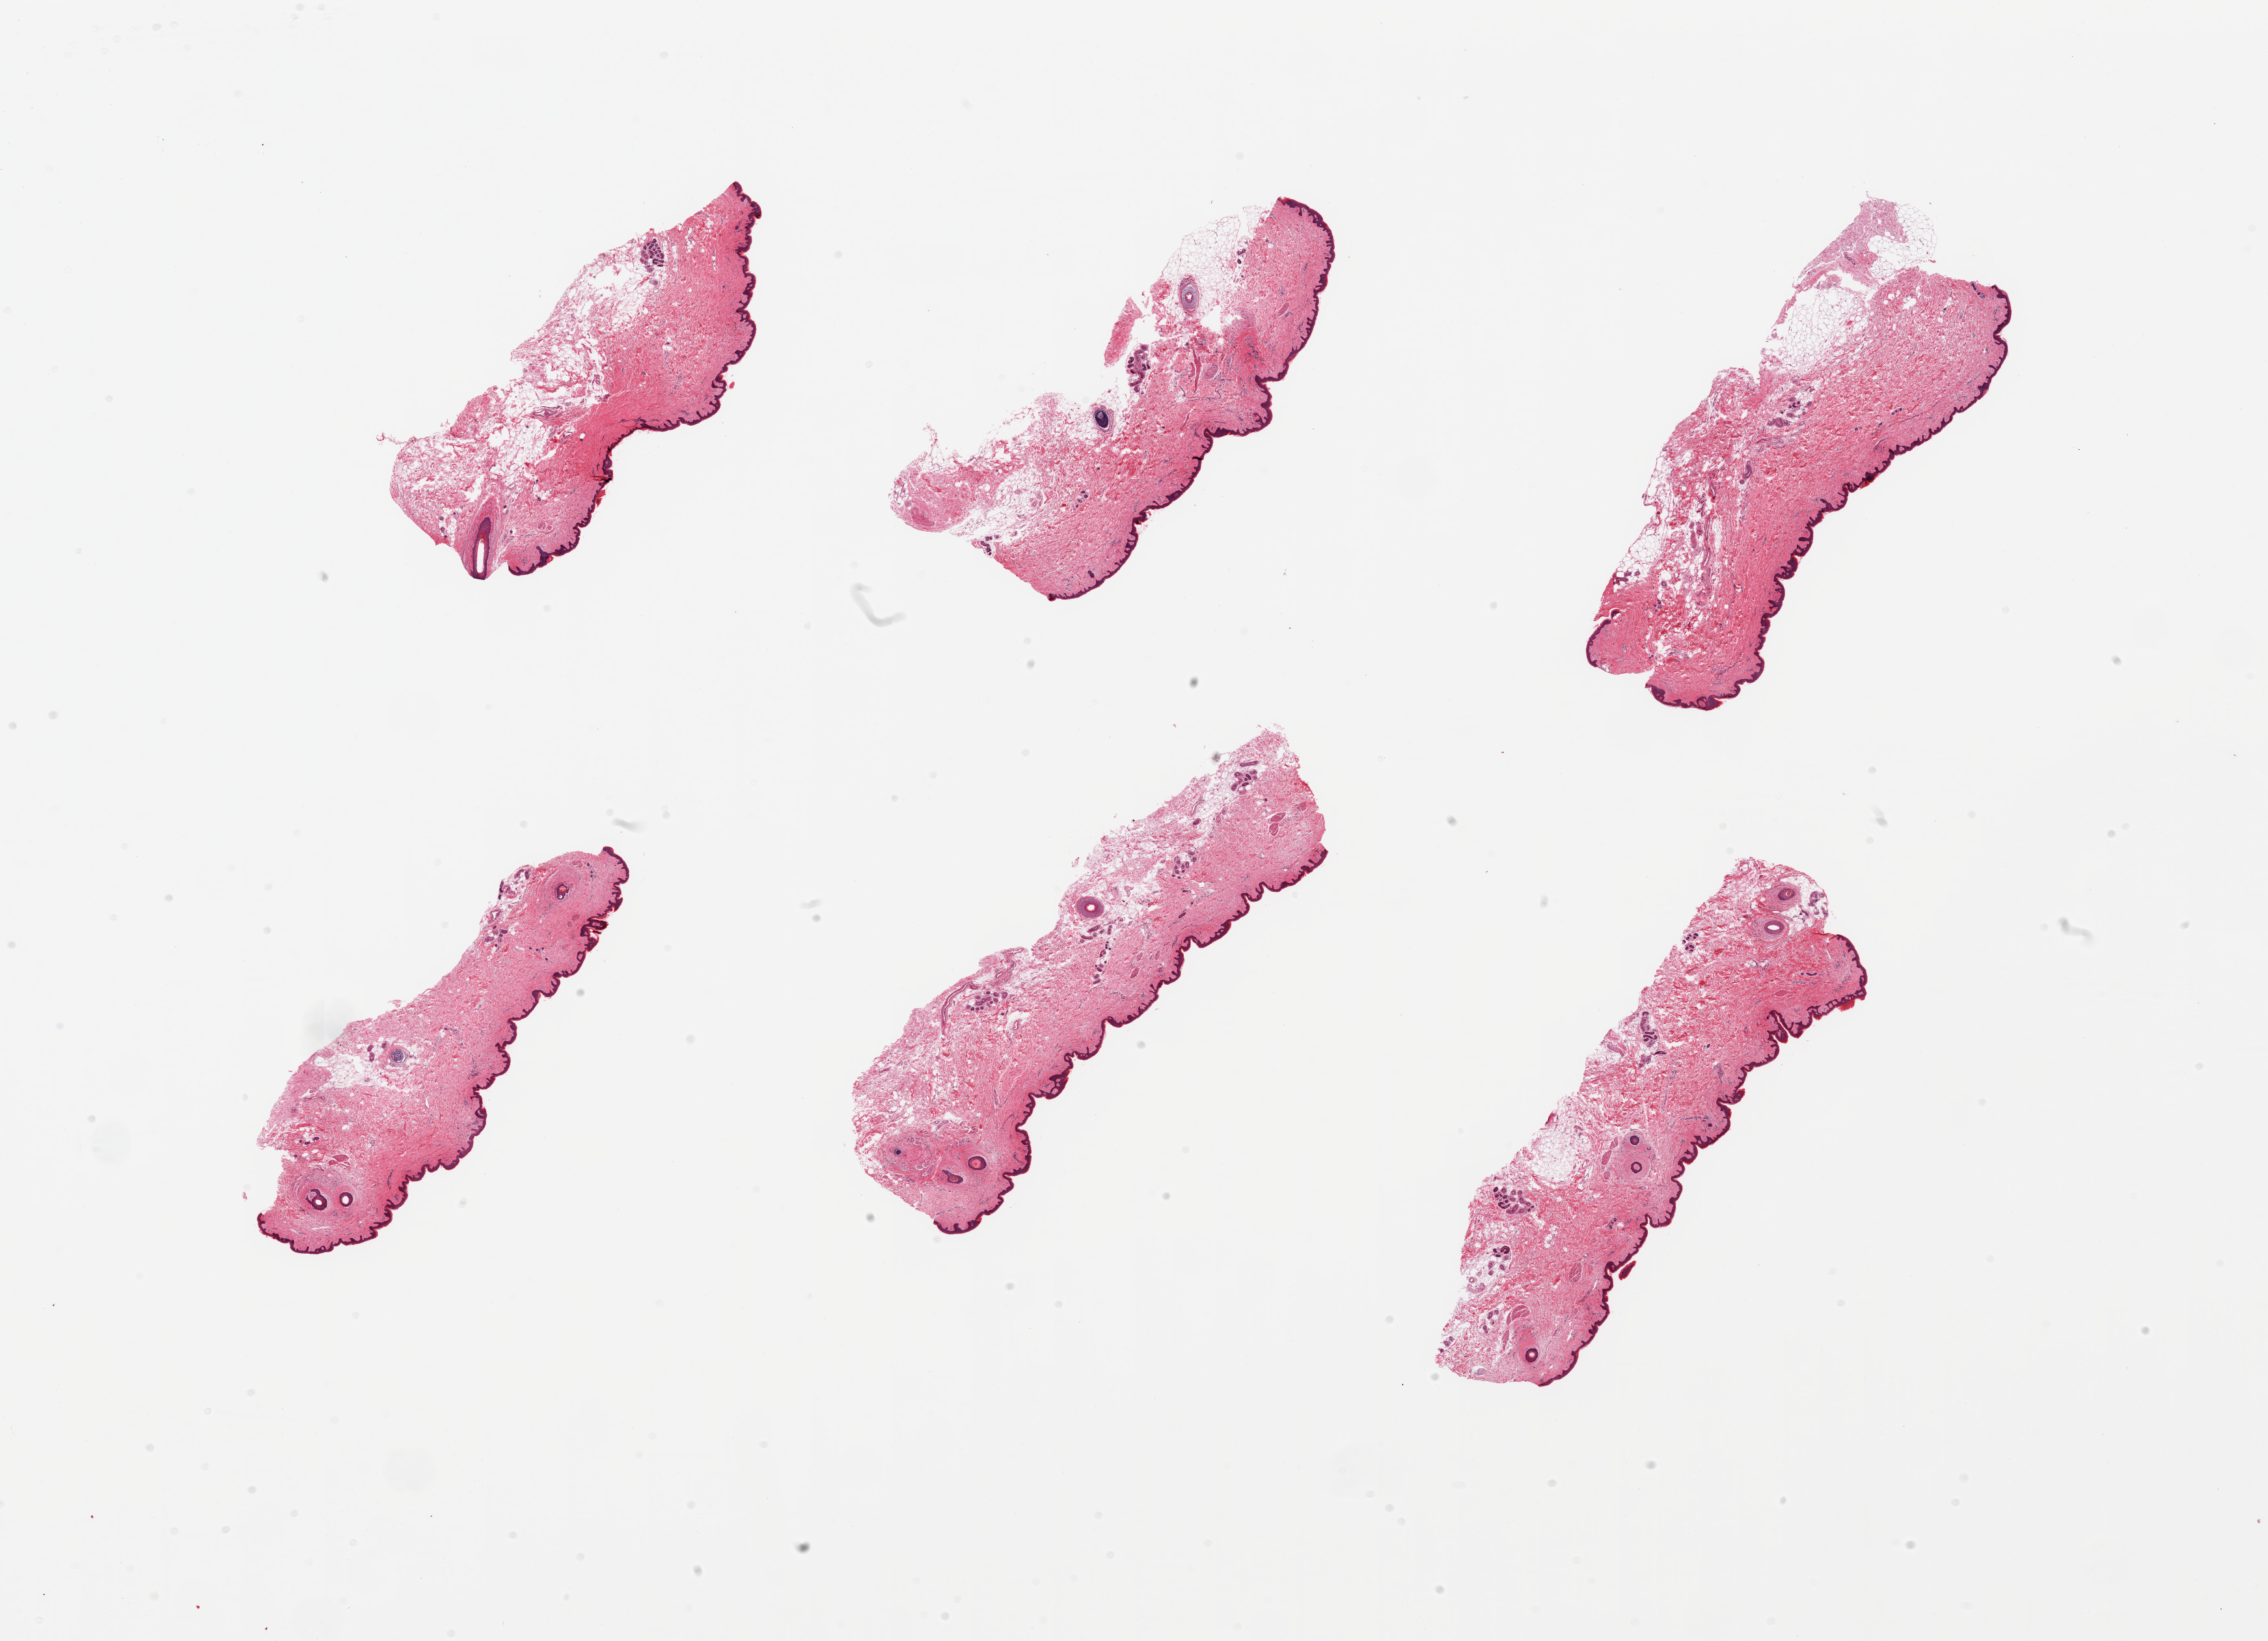
Hematoxylin and eosin (H&E) whole-slide image, brightfield — shown as a low-resolution overview of the whole scanned area (about 27.6 x 19.9 mm, from a 20x scan). PAXgene-fixed paraffin-embedded (PFPE) section. Section of skin of suprapubic region (target tissue). Tissue donor sample. Donor: female.
• reviewer comment on this tissue sample: 6 pieces, trace adherent fat; squamous epithelium is ~50 microns